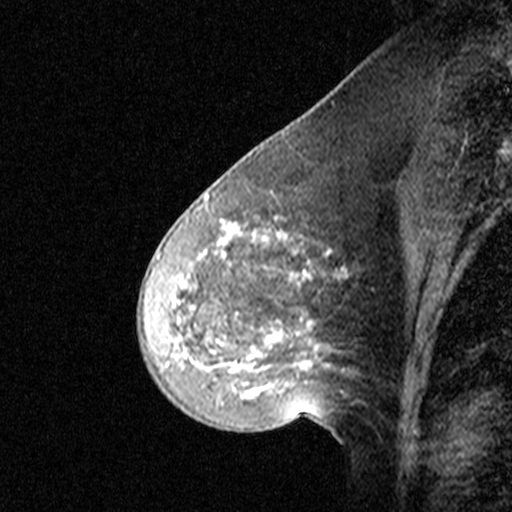
Breast MRI (dynamic contrast-enhanced), one sagittal slice. Position 17 of 44 along the scan axis. Dynamic contrast-enhanced study with each time point stored as its own series, time point 2 of 3 at this slice position (early post-contrast, ordered by acquisition time). 1.5 T. TE 4.5 ms, TR 11 ms. 3 mm slice thickness. 512 × 512 image matrix, field of view 200 × 200 mm. Patient: female, 46 years. Case-level facts recorded for this patient, not image findings: setting: breast cancer imaged before/during neoadjuvant chemotherapy; receptor status: HER2-positive.
Structures marked on this image (semi-automatic segmentation, software-assisted and operator-edited):
- analysis volume of interest (the breast-tissue region the enhancement analysis was run in; not a lesion): box from (x=144, y=172) to (x=359, y=393) px
- tumour enhancement mask (voxels above the 90 % enhancement threshold inside the analysis volume of interest): (x=178, y=189)–(x=346, y=372)